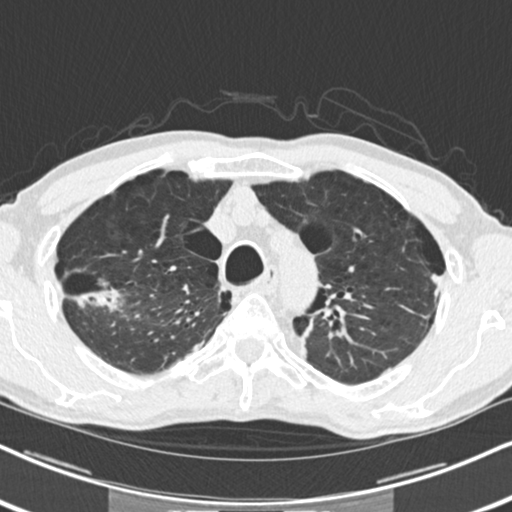
Axial slice from a low-dose chest CT screening exam; baseline screening round; lung window (W 1500 / L -600 HU); 120 kVp; slice 54 of 250 in the series. Male participant, aged 71 years at enrolment.
Expert-annotated lung lesion, box from (x=85, y=269) to (x=140, y=315) px. The screening reader recorded 2 non-calcified nodules or masses ≥4 mm on this exam; which of them this box marks is not recorded. Participant outcome: lung cancer diagnosed 454 days after this screen (after the second annual screen) — adenocarcinoma, NOS, right upper lobe, well differentiated (G1), stage IA (AJCC 6th edition), 30 mm at pathology.